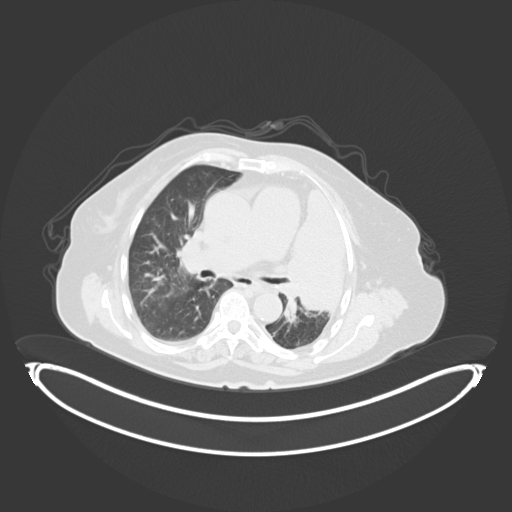
Chest CT, one axial slice. Position 203 of 284 along the scan axis. 120 kVp. Lung window (W 1500 / L -600 HU). 512 × 512 image matrix, field of view 500 × 500 mm. Female patient, age 75 years. From the clinical record (not read from this slice): clinical TNM (as recorded): T3 N3 M1.
Structures marked on this image (rectangle marked by the reading radiologist):
- lung tumour (recorded histology: adenocarcinoma): bounding box [x1, y1, x2, y2] px = [291, 188, 356, 316]